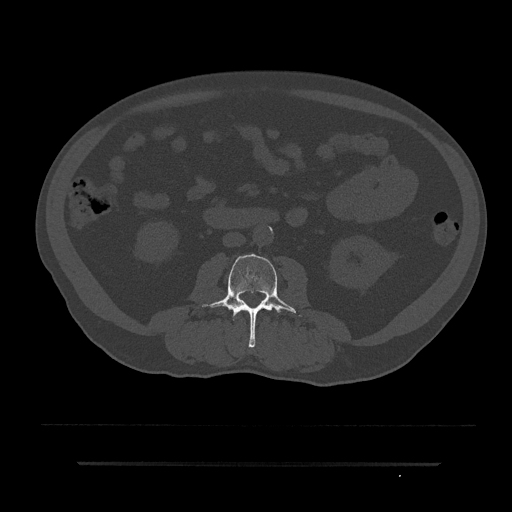
CT including the spine, one axial slice; slice 8 of 797 in the series (ordered by position); bone window (W 1800 / L 400 HU); 0.5 mm slice thickness; 512 × 512 image matrix. Patient: male, 59 years. Case-level facts recorded for this patient, not image findings: primary cancer: bile ducts; vertebrae with lytic lesions (as recorded): T10.
Outlined on this slice (semi-automatically segmented with operator editing):
- L2 vertebra: bounding box [x1, y1, x2, y2] px = [241, 309, 250, 313]
- L3 vertebra: [201, 254, 303, 348]